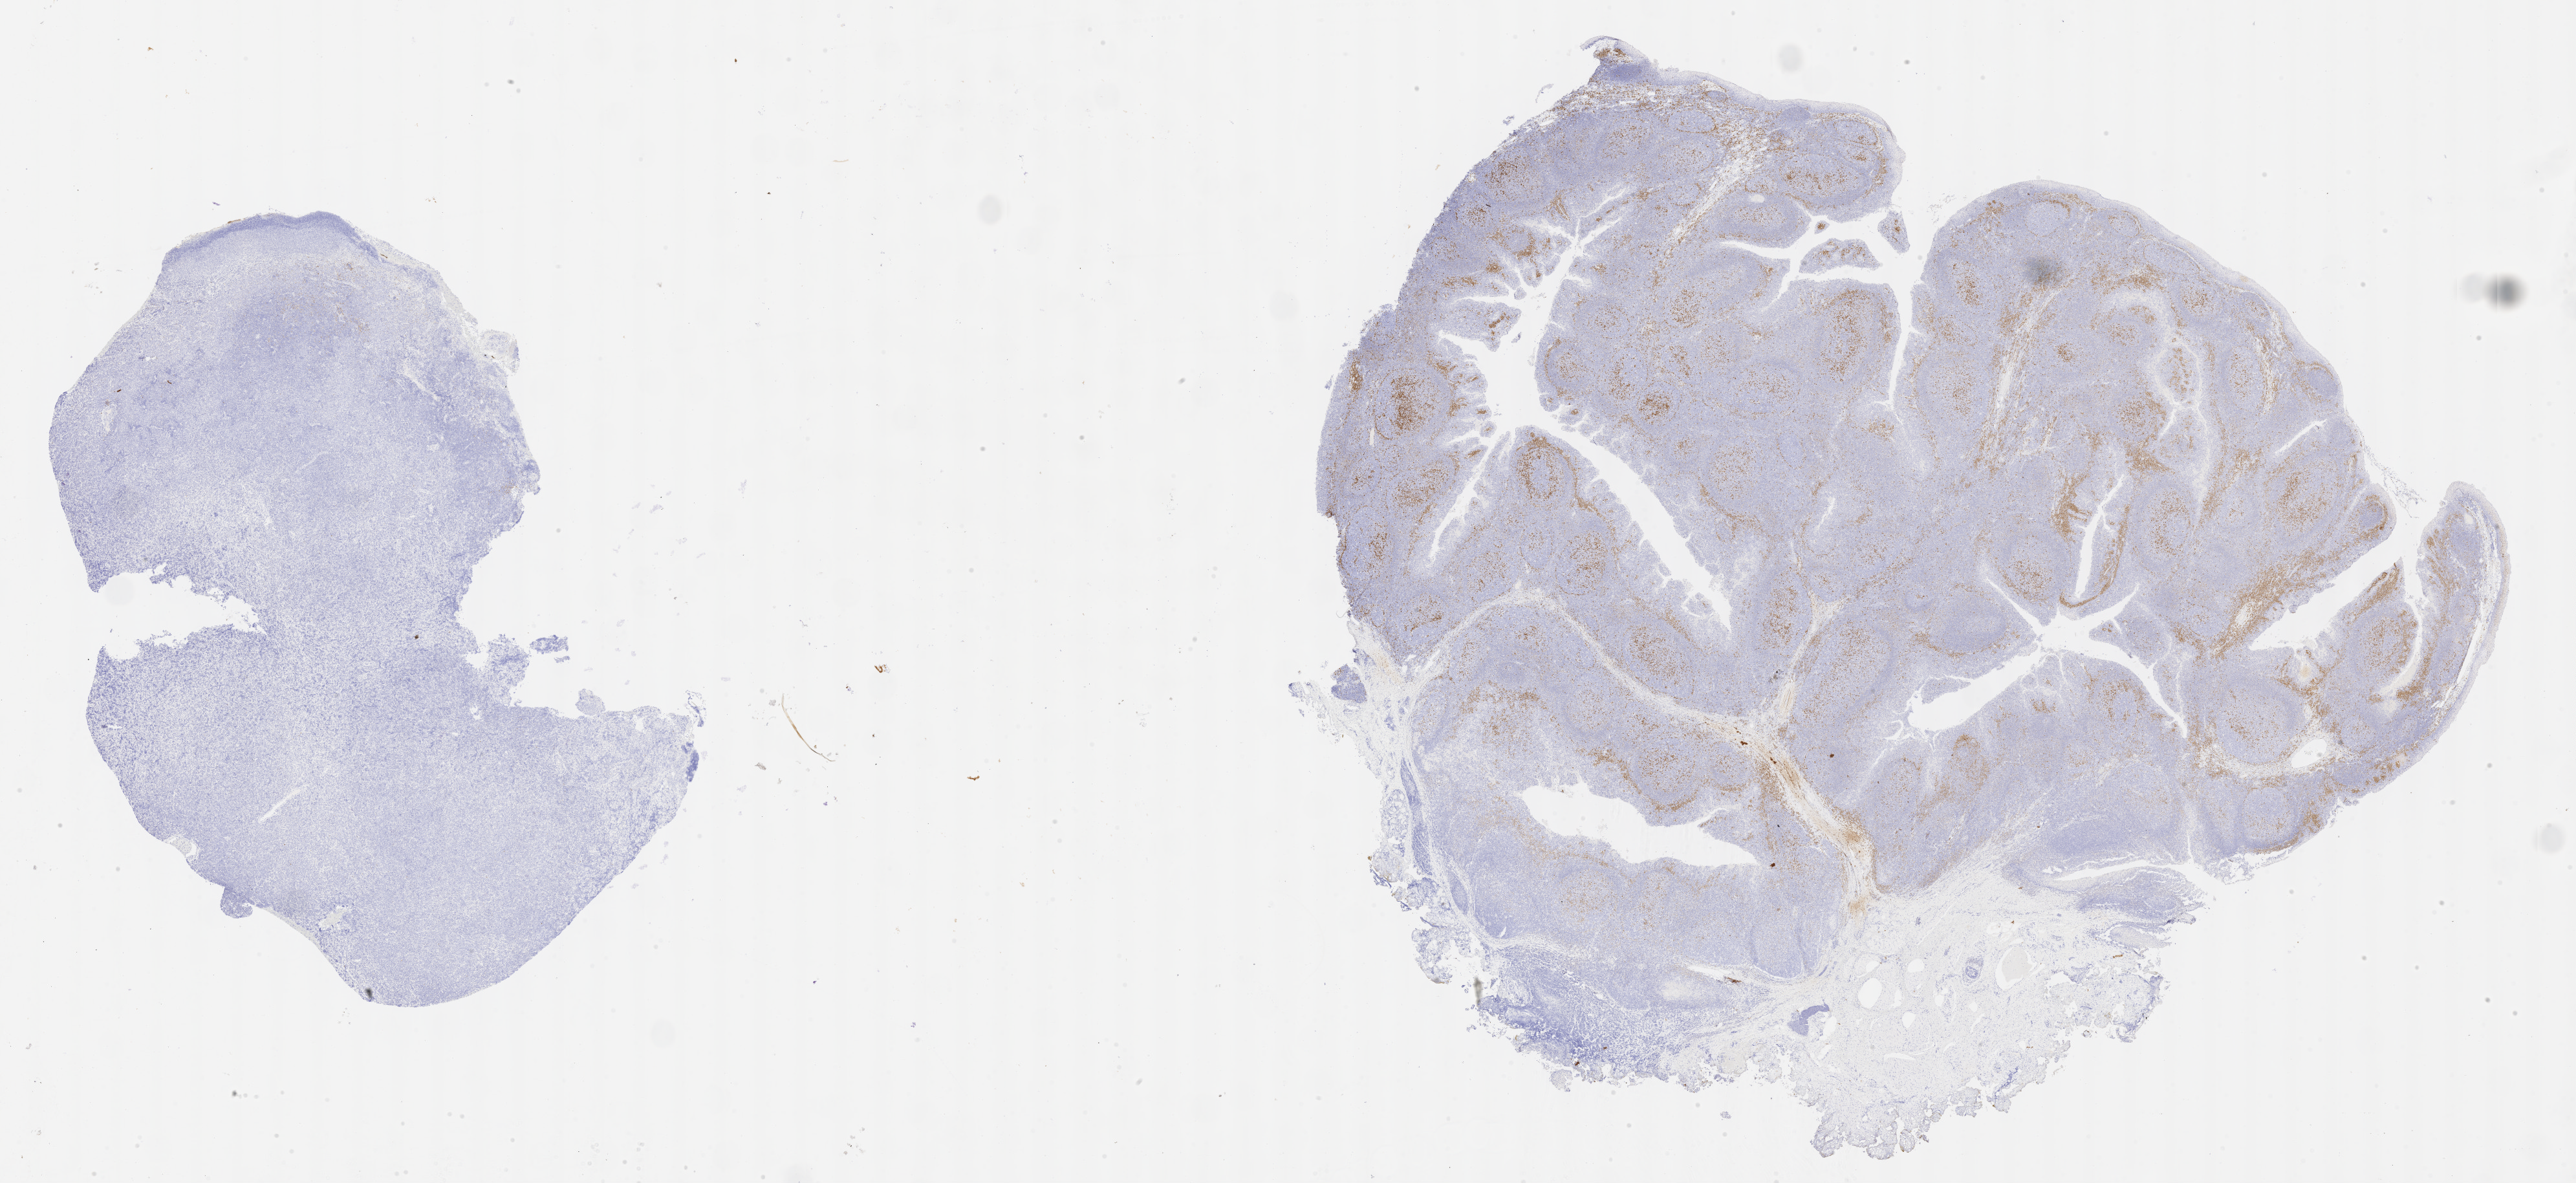
Immunohistochemistry (IHC) whole-slide image stained for IRF4/MUM1, low-resolution overview of the scanned area, about 32.2 x 14.8 mm. Tumor tissue. Male patient; age at initial diagnosis 7 years.
• diagnosis: Diffuse large B-cell lymphoma, NOS